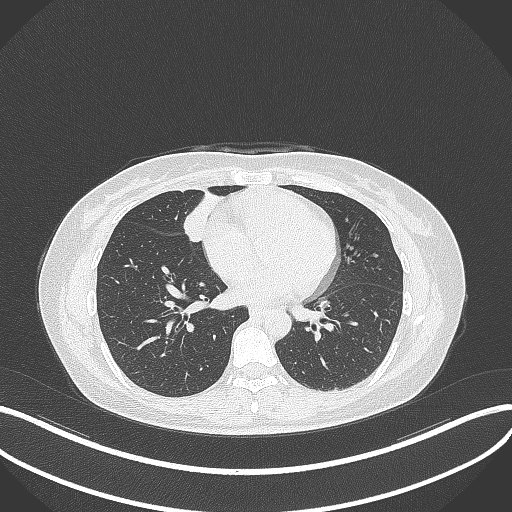
Chest CT, one axial slice. Slice 115 of 284 in the series (ordered by position). 120 kVp. Lung window (W 1500 / L -600 HU). 512 × 512 image matrix. Female patient, age 43 years. From the clinical record (not read from this slice): clinical TNM (as recorded): T1c N3 M1.
Annotated regions visible in this slice (bounding box drawn by a radiologist):
- lung tumour (recorded histology: adenocarcinoma): bounding box (x1, y1, x2, y2) in pixels: (184, 196, 214, 244)